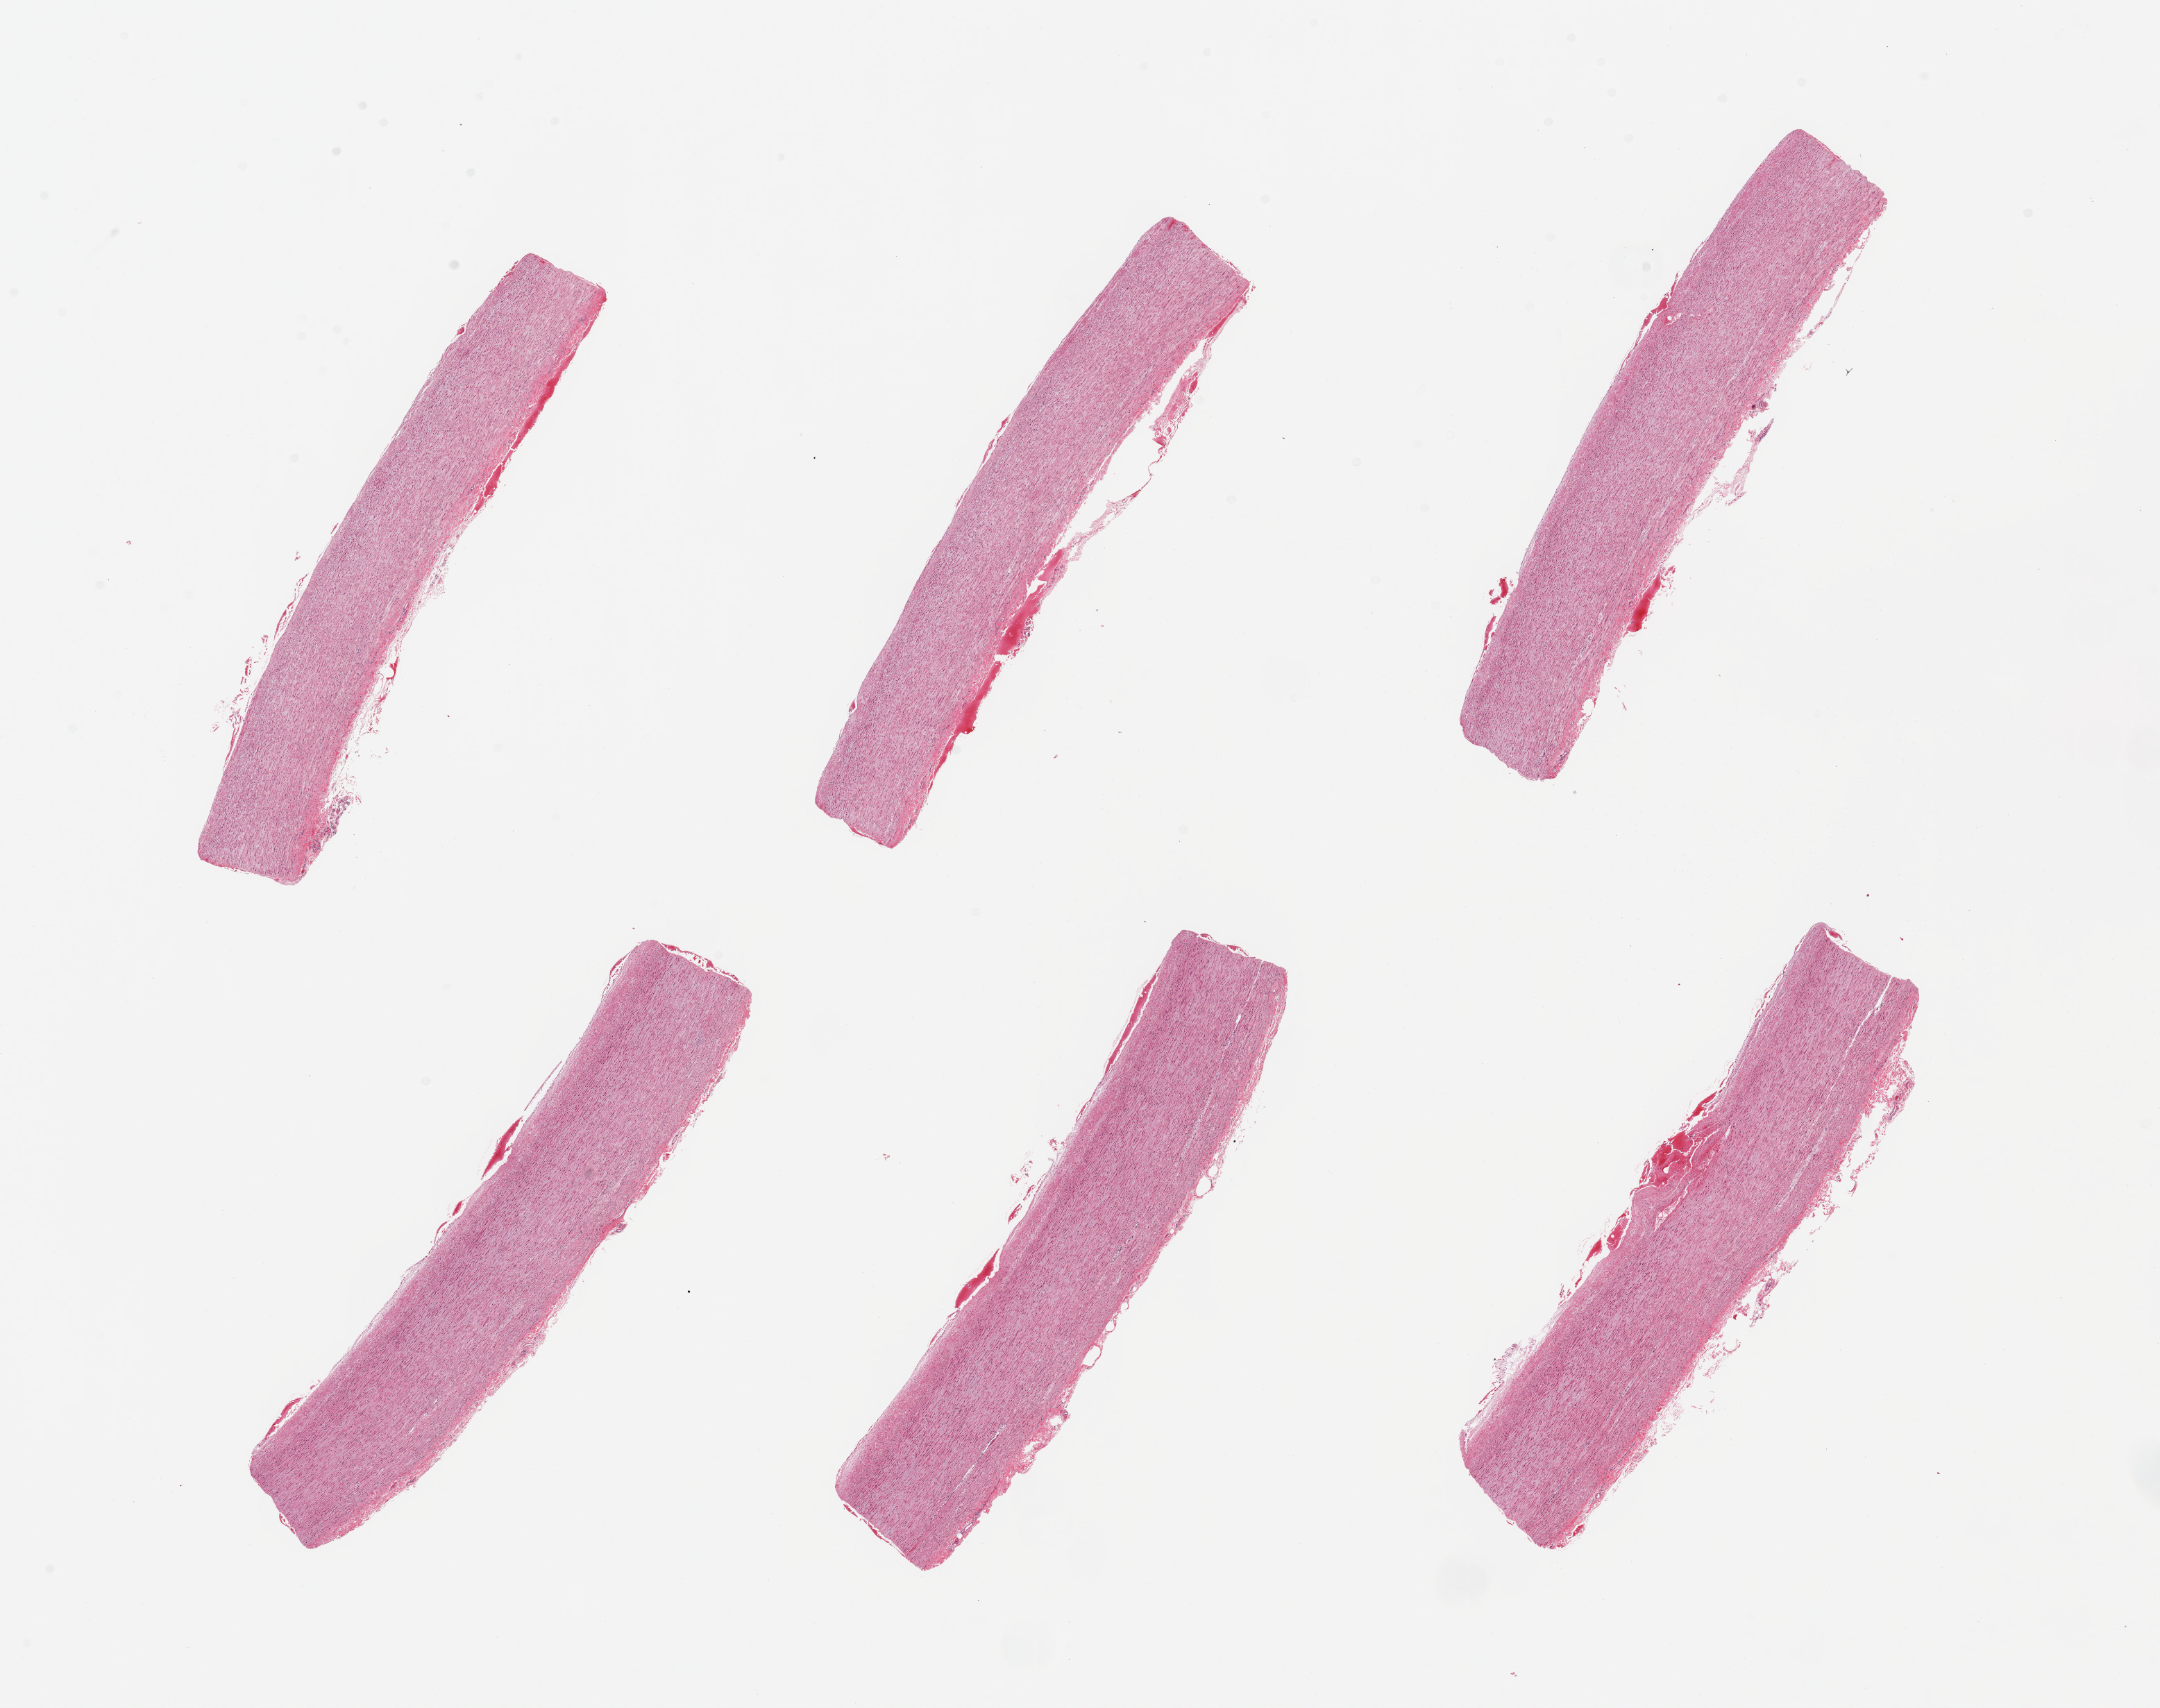
Digitized H&E-stained section — low-resolution overview of the scanned area, about 24.6 x 19.5 mm (slide scanned at 20x), PAXgene-fixed paraffin-embedded (PFPE) section, sampled site (target tissue): aorta, tissue donor sample. Donor sex: female.
Reviewer comment on this tissue sample: 6 pieces; no plaques.